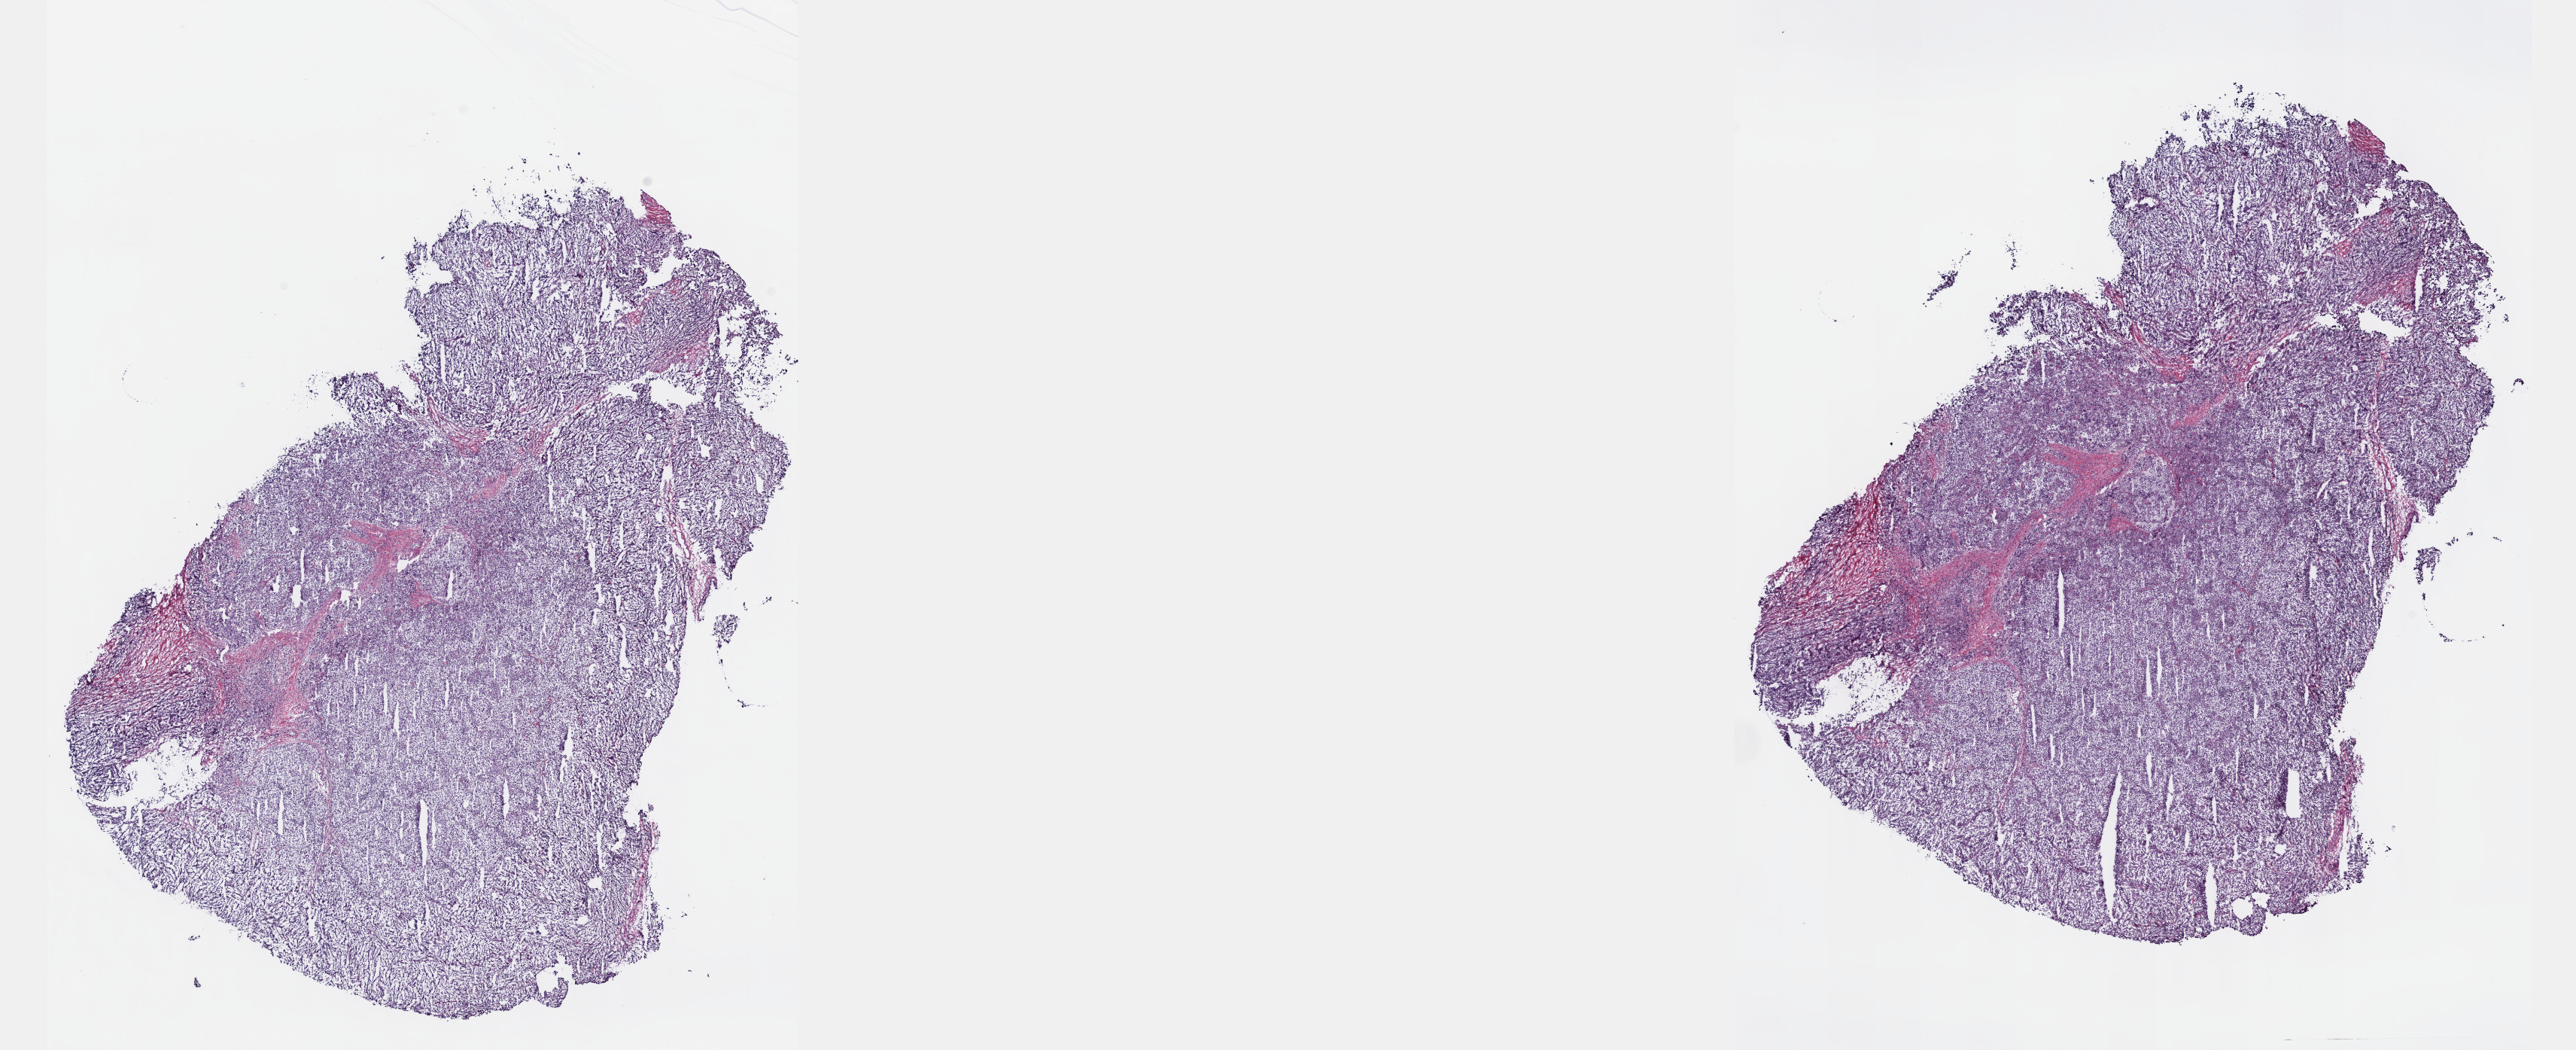
H&E whole-slide image — whole scanned area (about 27.7 x 11.3 mm, from a 40x scan) shown as a low-resolution overview, frozen section from the top of the tissue portion, testis, primary tumour sample. Patient: male, age at initial diagnosis 26 years. Pathologist review of this section (percent, as recorded): tumour cells 70%, tumour nuclei 70%, normal cells 0%, stromal cells 25%, necrosis 5%. Infiltration values recorded for this section: lymphocyte infiltration 40%, monocyte infiltration 20%, neutrophil infiltration 20%.
AJCC pathologic stage: IA (7th edition). Histologic diagnosis: Seminoma, NOS. Laterality: left.